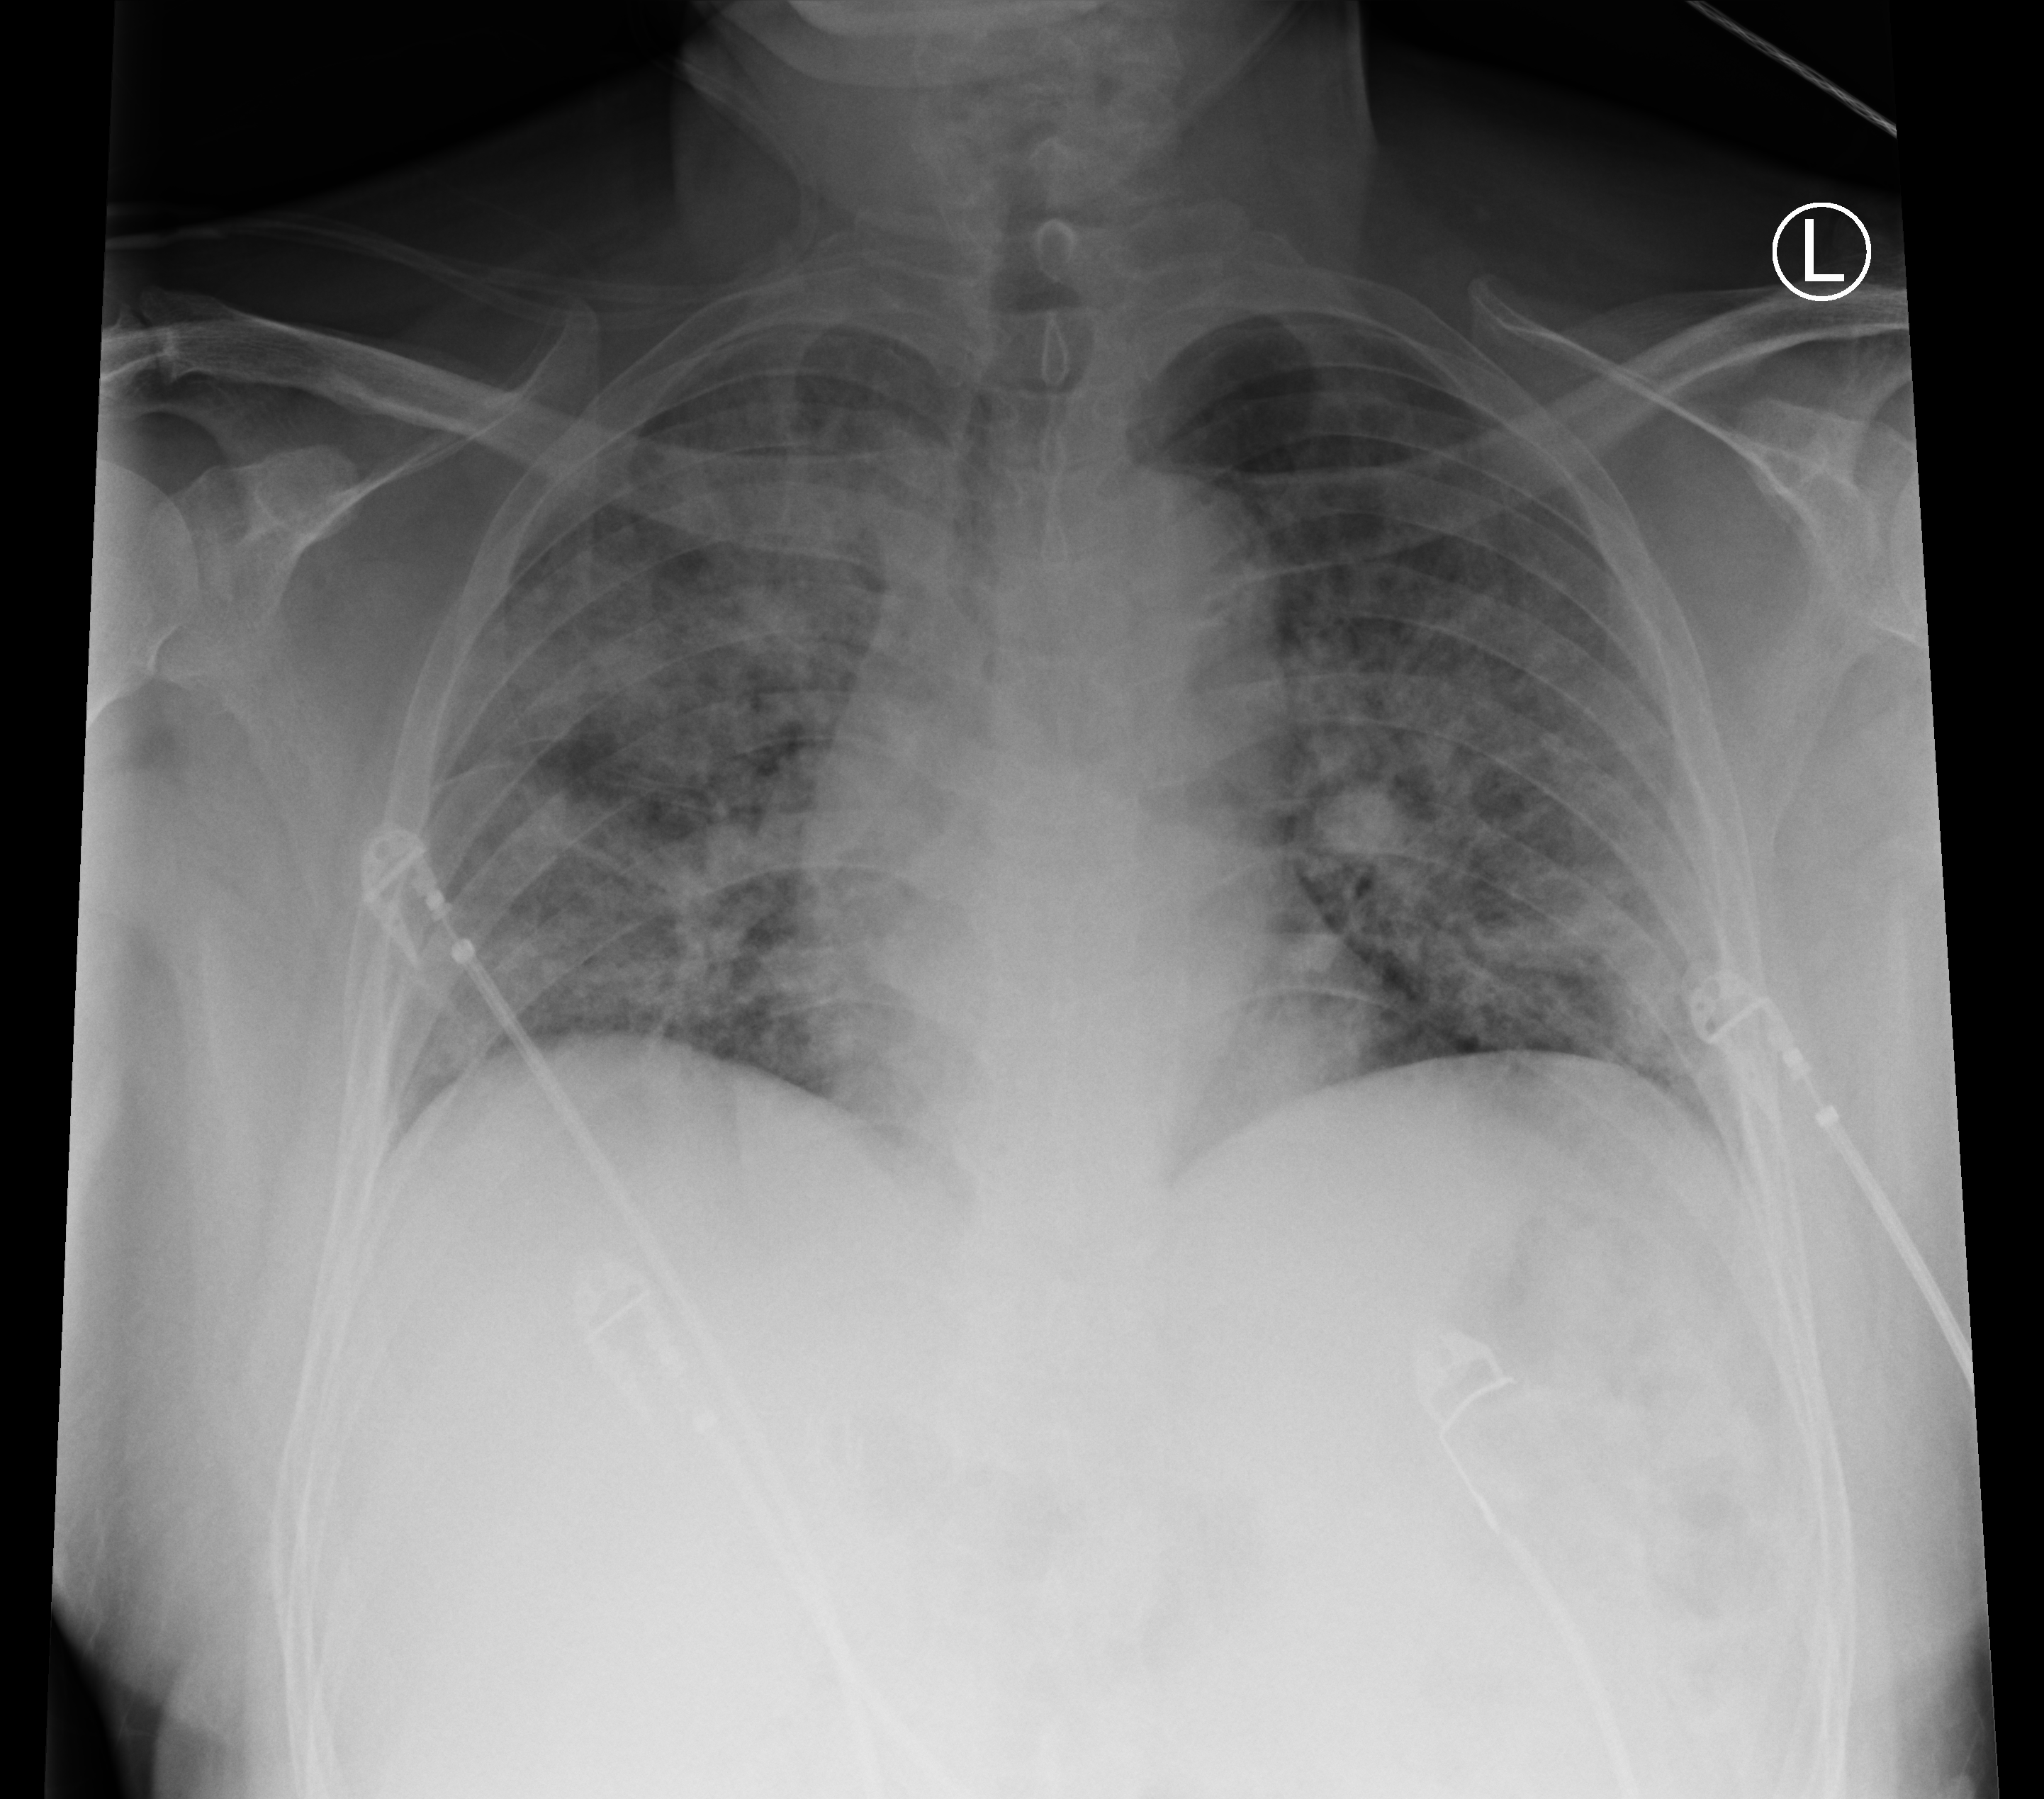
Portable chest radiograph; anteroposterior (AP) projection. Male patient hospitalised with COVID-19, age 60–74 years.
Admission-level facts for this patient (not findings on this image; timing relative to this image not recorded): admitted to intensive care during this hospital stay: yes; mechanically ventilated during this hospital stay: yes.